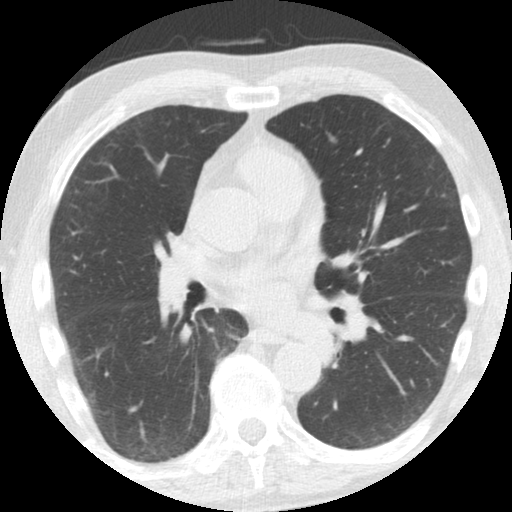
Chest CT (low-dose screening protocol), one axial image, third annual screen, lung window (W 1500 / L -600 HU), 2.5 mm slice thickness, standard (soft-tissue) reconstruction kernel (STANDARD), 120 kVp, 512 × 512 image matrix. Male participant, aged 61 years at enrolment. Former smoker at enrolment.
Expert-annotated lung lesion, bounding box (x1, y1, x2, y2) in pixels: (295, 316, 344, 362). Screening reader's record for this exam: no non-calcified nodule ≥4 mm recorded. Participant outcome: lung cancer diagnosed 363 days after this screen — squamous cell carcinoma, NOS, left upper lobe, left lower lobe, well differentiated (G1), stage IIB (AJCC 6th edition), 100 mm at pathology.